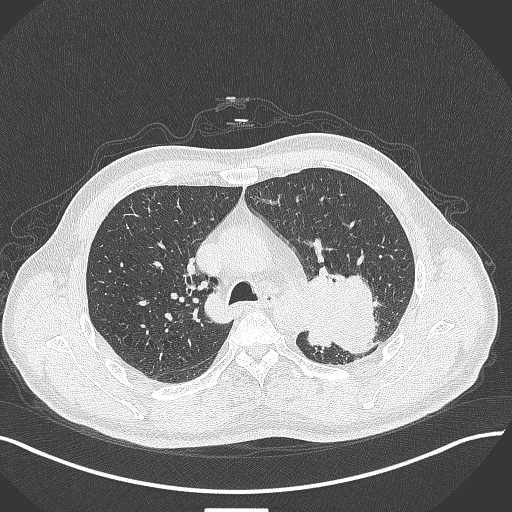
Chest CT, one axial slice. Slice 291 of 429 in the series (ordered by position). Reconstruction kernel B70f. Lung window (W 1500 / L -600 HU). 1 mm slice thickness. 512 × 512 image matrix, field of view 400 × 400 mm. Patient: male, 55 years. Case-level facts recorded for this patient, not image findings: clinical TNM (as recorded): T3 N0 M1c; histopathological grade: G3.
Structures marked on this image (rectangle marked by the reading radiologist):
- lung tumour (recorded histology: adenocarcinoma): box from (x=305, y=271) to (x=380, y=353) px